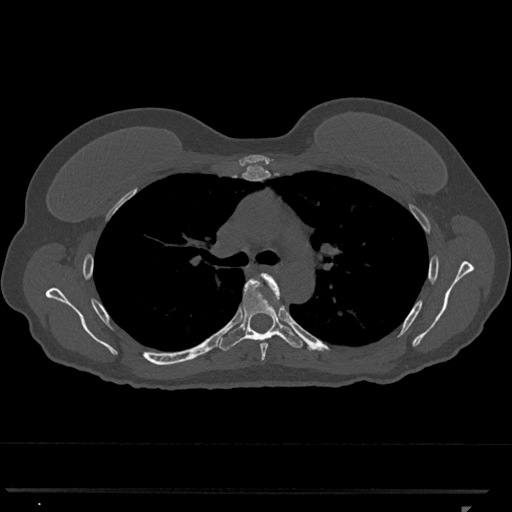
CT including the spine, one axial slice. Position 778 of 793 along the scan axis. Reconstruction kernel Br40s/3. Bone window (W 1800 / L 400 HU). 0.5 mm slice thickness. 512 × 512 image matrix, field of view 380 × 380 mm. Patient: female, 62 years. From the clinical record (not read from this slice): primary cancer: renal.
Structures marked on this image (semi-automatic segmentation, software-assisted and operator-edited):
- T5 vertebra: box from (x=260, y=274) to (x=281, y=361) px
- T6 vertebra: (x=219, y=277)–(x=303, y=351)